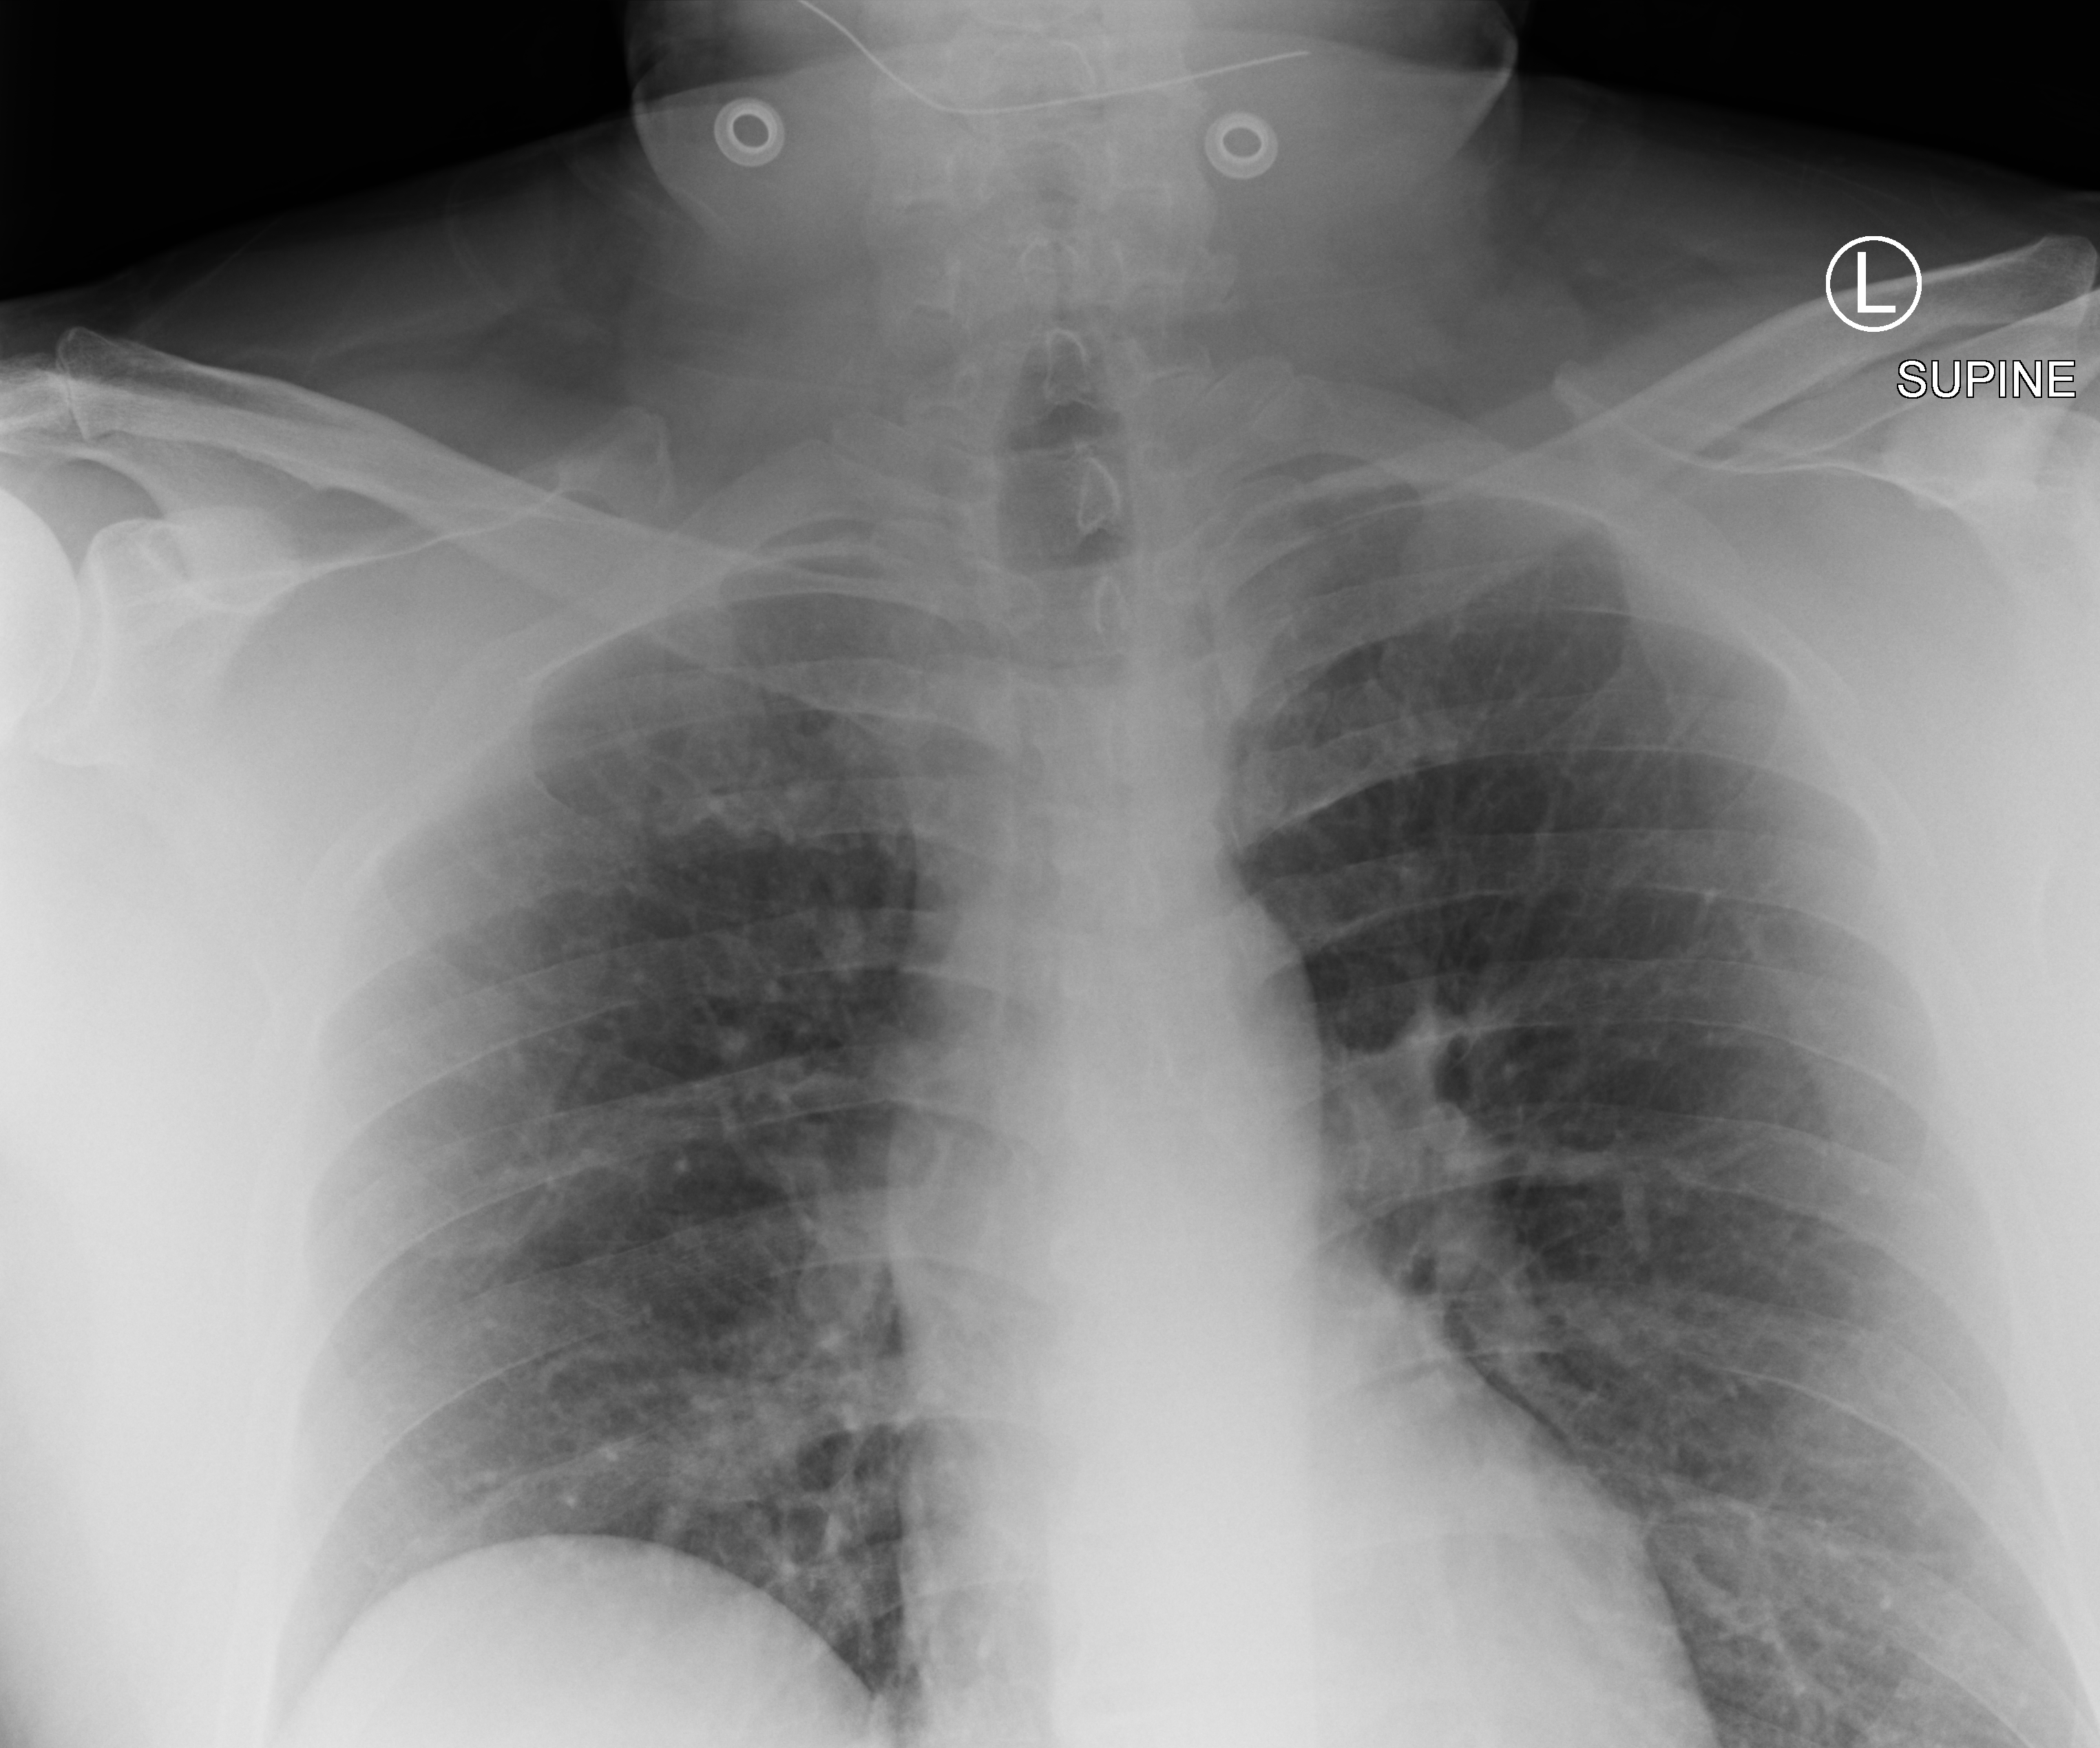
Portable chest radiograph, anteroposterior (AP) projection. Male patient hospitalised with COVID-19, age 18–59 years.
Admission-level facts for this patient (not findings on this image; timing relative to this image not recorded): mechanically ventilated during this hospital stay: no; admitted to intensive care during this hospital stay: no.